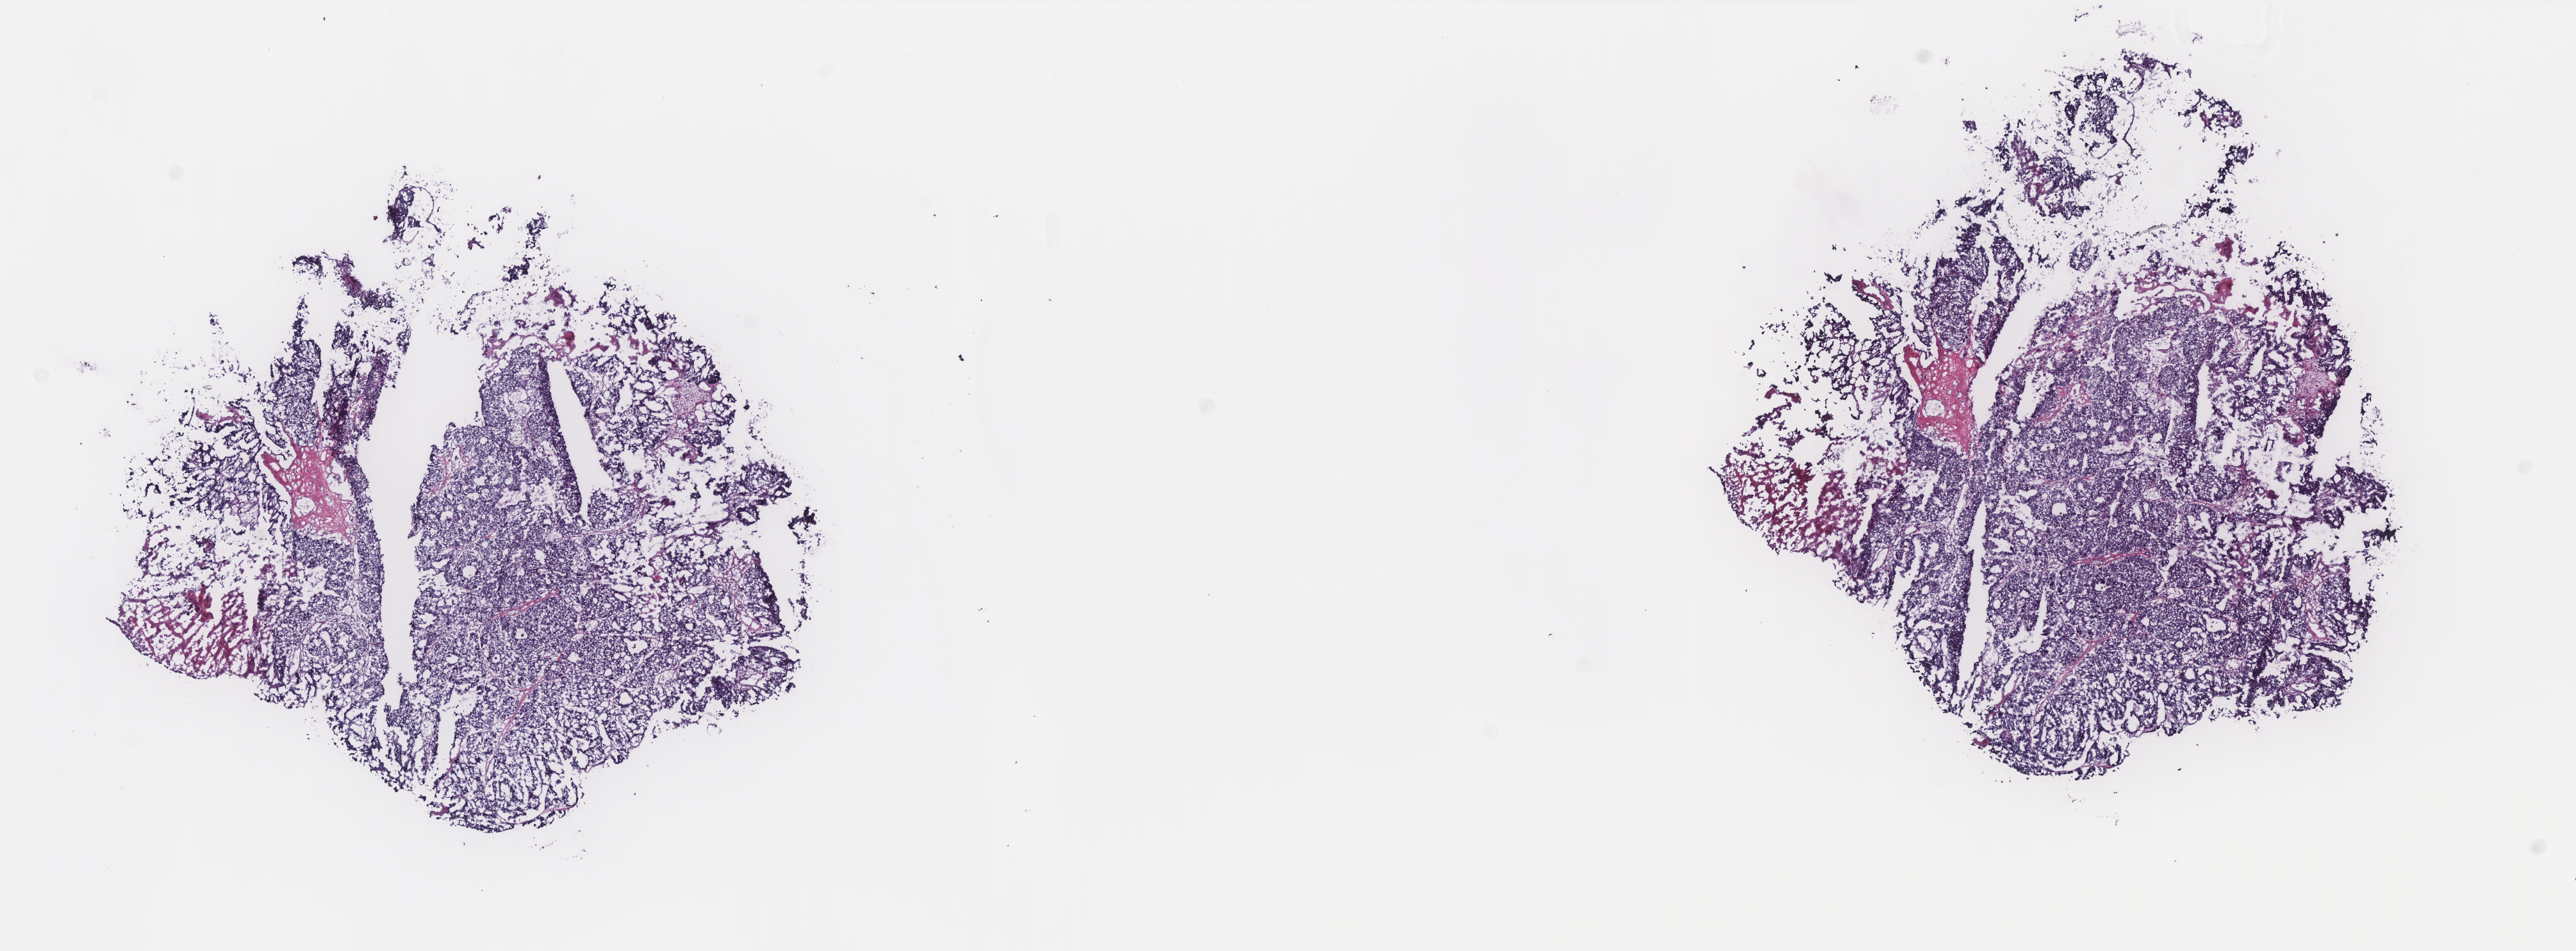
H&E-stained whole-slide image, a low-resolution overview of the entire scanned area, about 16.1 x 5.9 mm (slide scanned at 40x), frozen section from the top of the tissue portion, sample: primary tumour, uterus. Female, age 83 years at initial diagnosis. Histologic grade: G3 (poorly differentiated). Slide review estimates, as recorded: tumour cells 70%, tumour nuclei 90%, normal cells 0%, stromal cells 10%, necrosis 20%. Infiltration values recorded for this section: lymphocyte infiltration 10%, monocyte infiltration 0%, neutrophil infiltration 10%.
Histologic diagnosis: Endometrioid adenocarcinoma, NOS (endometrium). FIGO stage: IB.